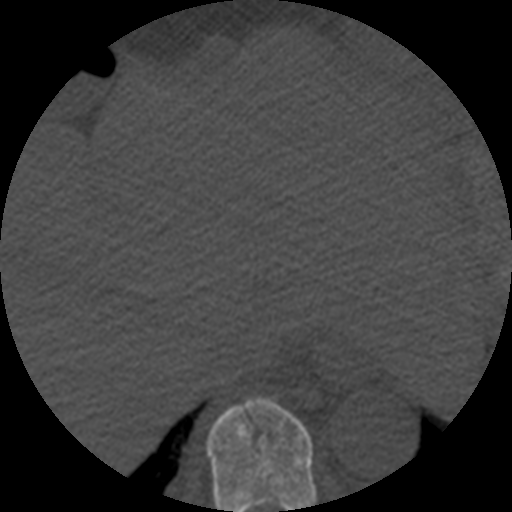
CT including the spine, one axial slice. Slice 290 of 508 in the series (ordered by position). Reconstruction kernel STANDARD. 120 kVp. Bone window (W 1800 / L 400 HU). 1.25 mm slice thickness. 512 × 512 image matrix, field of view 160 × 160 mm. Patient age 57 years. From the clinical record (not read from this slice): primary cancer: prostate.
Annotated regions visible in this slice (semi-automatic segmentation, software-assisted and operator-edited):
- T9 vertebra: box from (x=206, y=398) to (x=317, y=512) px